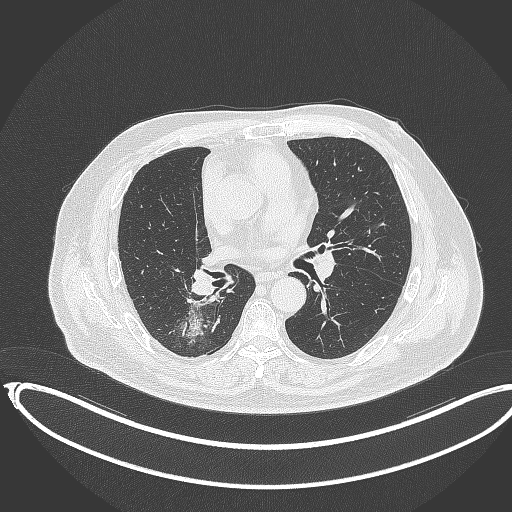
Chest CT, one axial slice. Slice 184 of 403 in the series (ordered by position). Reconstruction kernel B70f. Lung window (W 1500 / L -600 HU). 1 mm slice thickness. 512 × 512 image matrix, field of view 436 × 436 mm. Patient: male, 68 years. Case-level facts recorded for this patient, not image findings: clinical TNM (as recorded): T2a N0 M0.
Outlined on this slice (bounding box drawn by a radiologist):
- lung tumour (recorded histology: adenocarcinoma): bounding box [x1, y1, x2, y2] px = [168, 297, 210, 336]